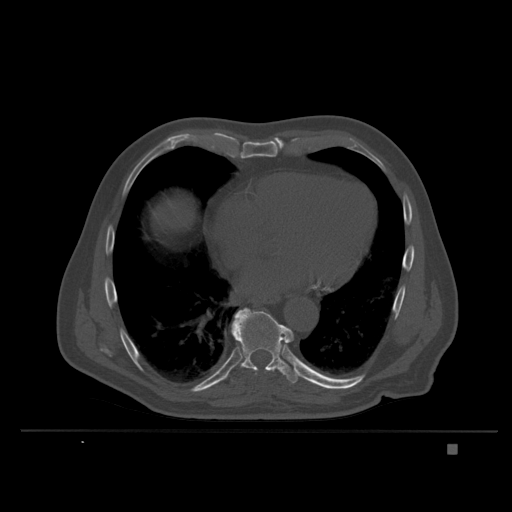
CT including the spine, one axial slice; slice 218 of 435 in the series (ordered by position); bone window (W 1800 / L 400 HU); 1.5 mm slice thickness; 512 × 512 image matrix, field of view 434 × 434 mm. Male patient, age 73 years. From the clinical record (not read from this slice): primary cancer: skin.
Outlined on this slice (semi-automatically segmented with operator editing):
- T9 vertebra: bounding box [x1, y1, x2, y2] px = [226, 308, 300, 384]